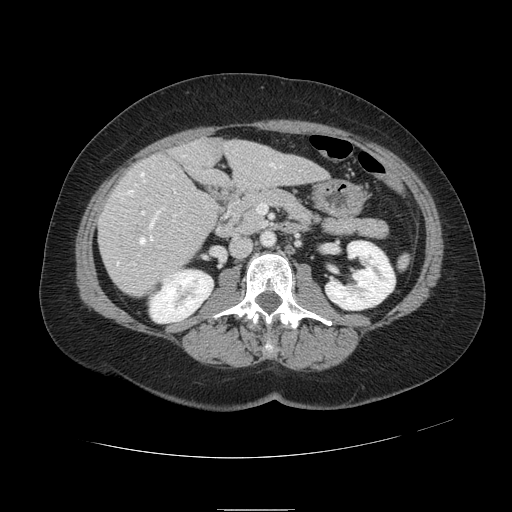
Contrast-enhanced abdominal CT, one axial slice; position 37 of 121 along the scan axis; 120 kVp; intravenous contrast given; soft-tissue window (W 400 / L 40 HU); 2.5 mm slice thickness; 512 × 512 image matrix, field of view 400 × 400 mm. Female patient, age 52 years. From the clinical record (not read from this slice): diagnosis: colorectal cancer liver metastases, imaged before liver resection.
Annotated regions visible in this slice (outlined manually by an expert reader):
- hepatic veins: bounding box <117,156,275,266> (left, top, right, bottom; pixels)
- liver: <99,138,326,296>
- planned liver remnant (the part of the liver to remain after resection): <176,138,326,187>
- portal vein (with intrahepatic branches): <142,211,176,217>